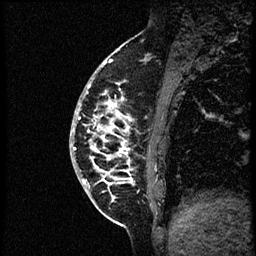
Breast MRI (dynamic contrast-enhanced), one sagittal slice; position 19 of 56 along the scan axis; dynamic contrast-enhanced study with each time point stored as its own series, time point 2 of 3 at this slice position (early post-contrast, ordered by acquisition time); 1.5 T; TE 4.2 ms, TR 21.3 ms; 2 mm slice thickness; 256 × 256 image matrix. Female patient, age 41 years. Case-level facts recorded for this patient, not image findings: setting: breast cancer imaged before/during neoadjuvant chemotherapy; receptor status: HER2-positive.
Structures marked on this image (semi-automatically segmented with operator editing):
- analysis volume of interest (the breast-tissue region the enhancement analysis was run in; not a lesion): box from (x=70, y=73) to (x=167, y=205) px
- tumour enhancement mask (voxels above the 100 % enhancement threshold inside the analysis volume of interest): (x=74, y=82)–(x=133, y=200)